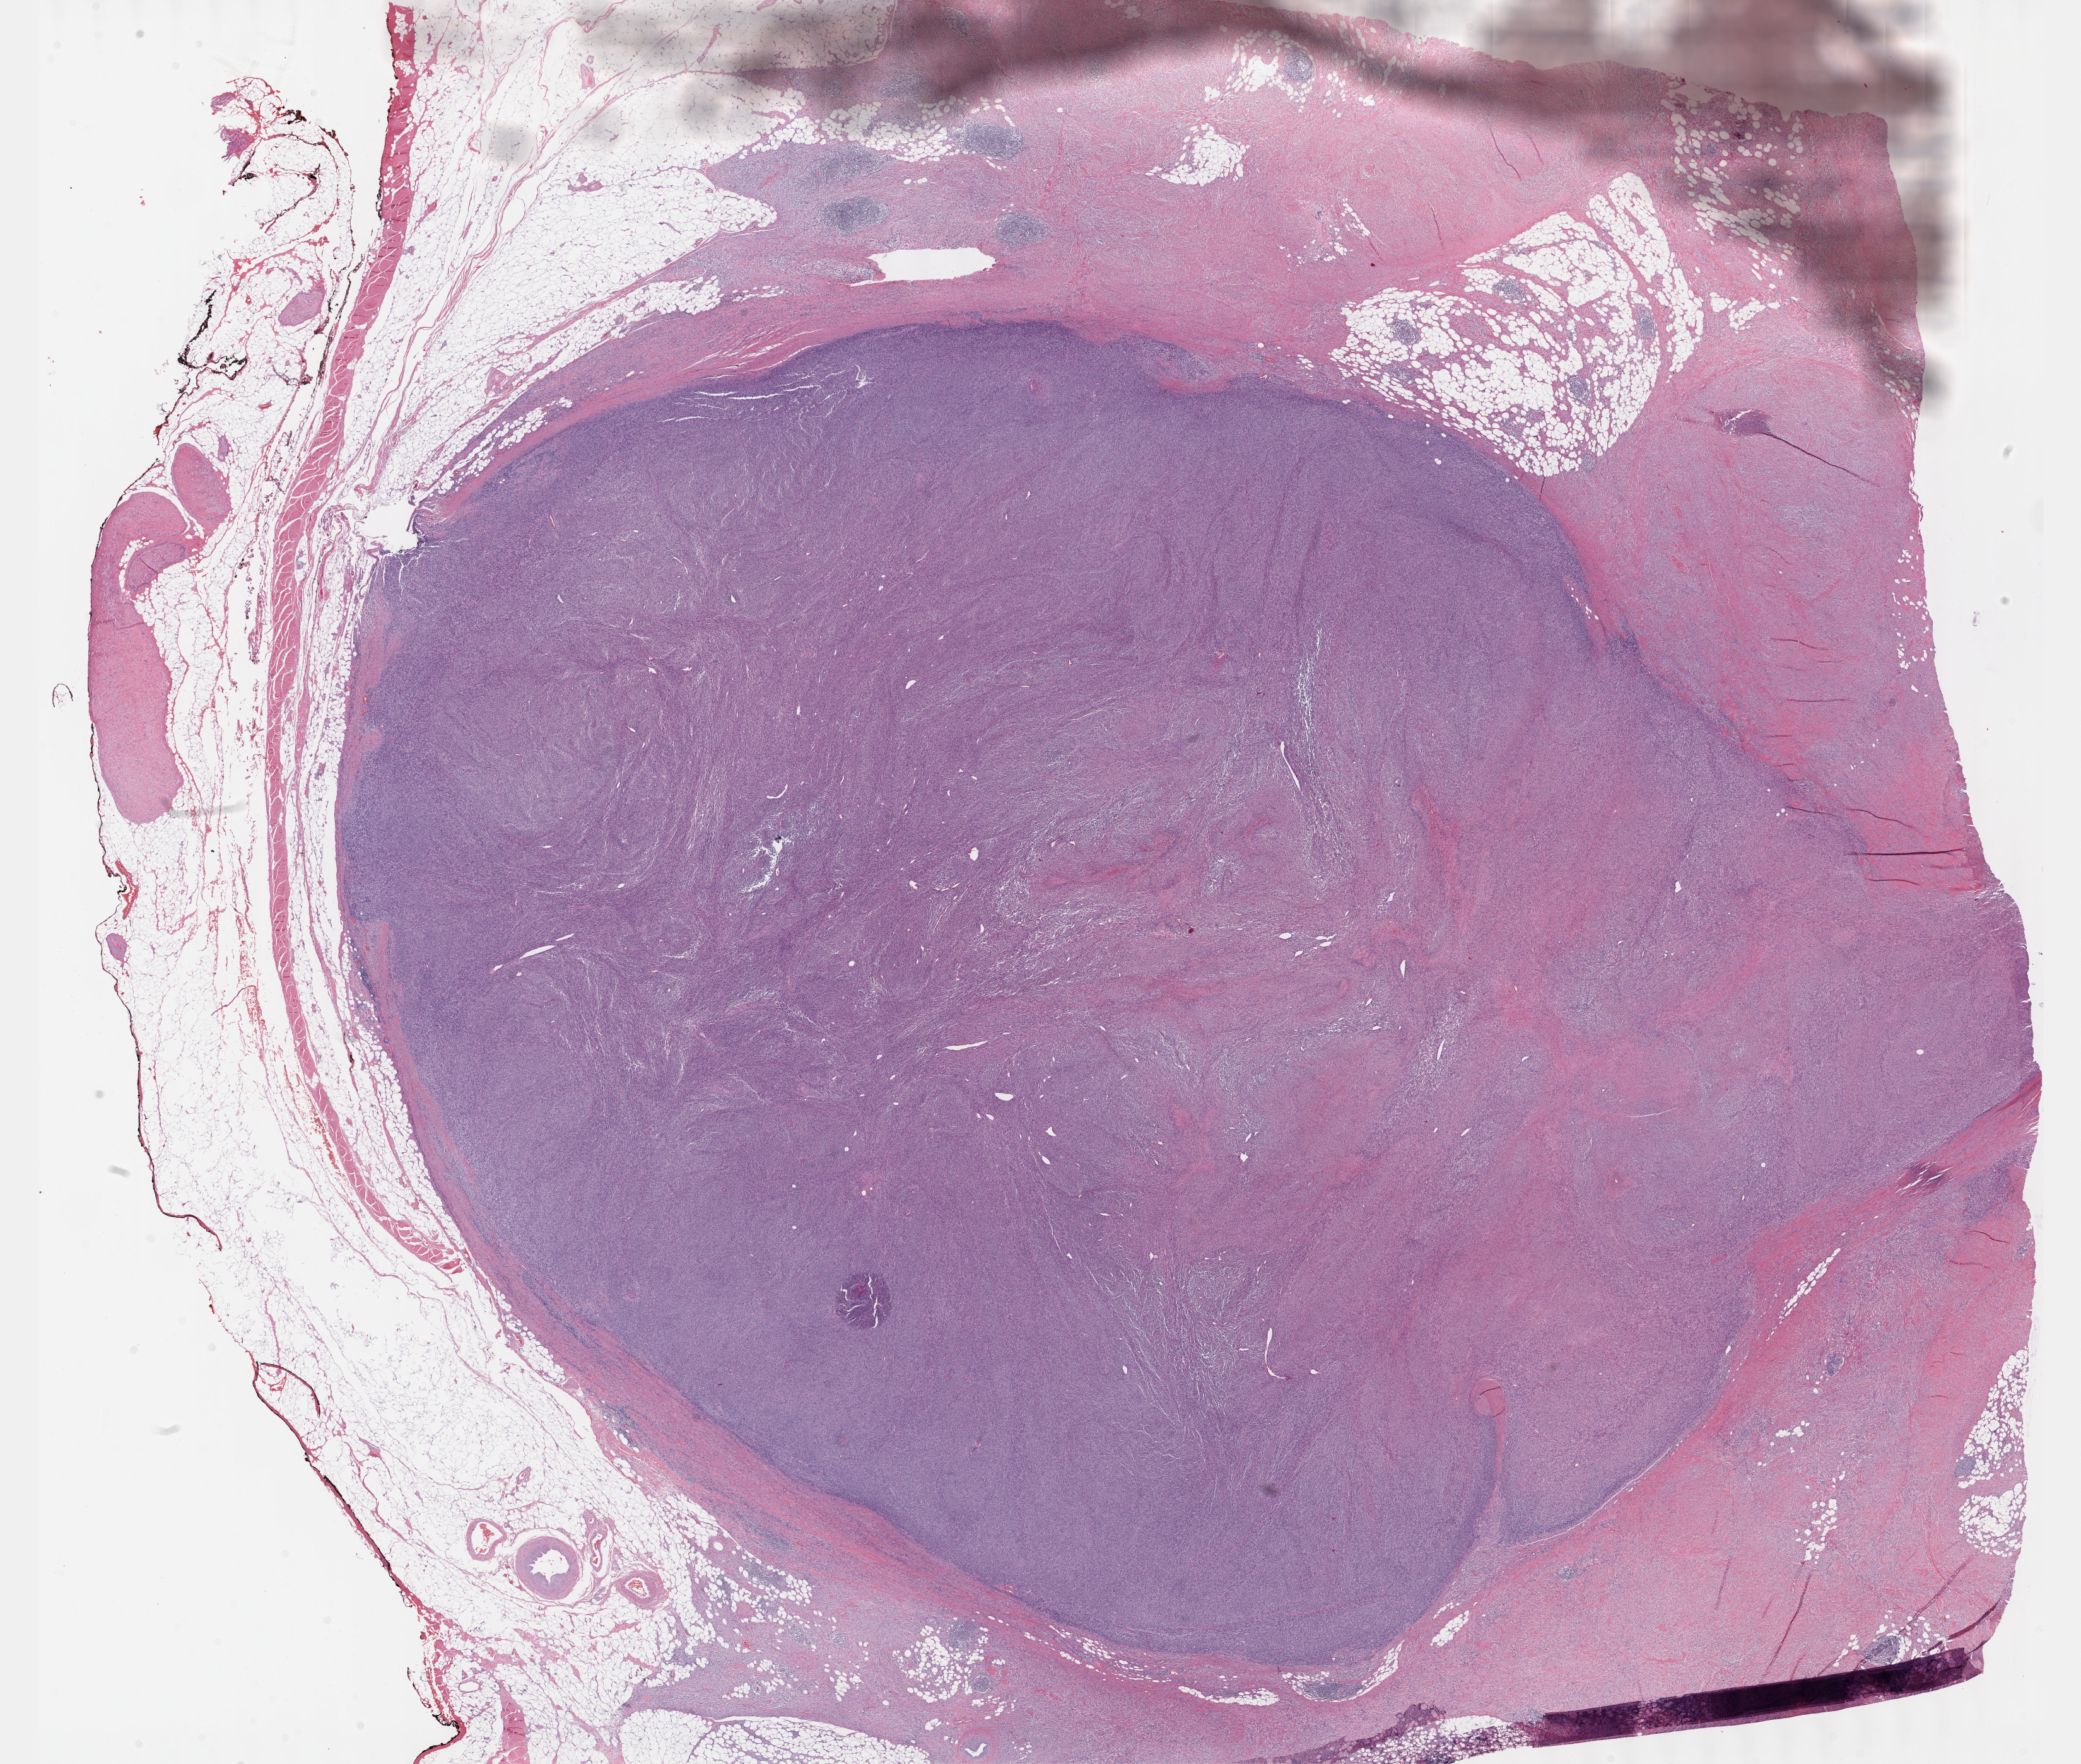
Digitized H&E-stained tissue section (whole slide), shown as a low-resolution overview of the whole scanned area (about 26.7 x 22.6 mm, acquisition: 40x scan); formalin-fixed paraffin-embedded (FFPE) diagnostic section; connective, subcutaneous and other soft tissues, primary tumour sample. Male patient; age at initial diagnosis 52 years.
* histologic diagnosis: Malignant peripheral nerve sheath tumor (connective, subcutaneous and other soft tissues of trunk, NOS)